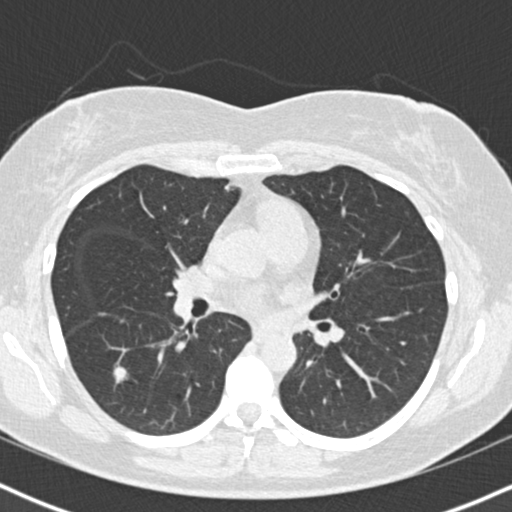
Chest CT (low-dose screening protocol), one axial image, first (baseline) screen, lung window (W 1500 / L -600 HU), 2 mm slice thickness, slice 75 of 167 in the series, 512 × 512 image matrix, field of view 320 × 320 mm. Female, age 55 years at enrolment. Former smoker at enrolment.
Lesion marked by an expert reader, bounding box [x1, y1, x2, y2] px = [91, 347, 145, 396]. Screening reader's record for this exam (one nodule recorded; not confirmed to be the boxed lesion): non-calcified nodule or mass ≥4 mm, right lower lobe, 8 × 8 mm, poorly defined margins, soft tissue attenuation. Participant outcome: lung cancer diagnosed 14 days after this screen — bronchiolo-alveolar adenocarcinoma, NOS, right lower lobe, well differentiated (G1), stage IA (AJCC 6th edition), 12 mm at pathology.